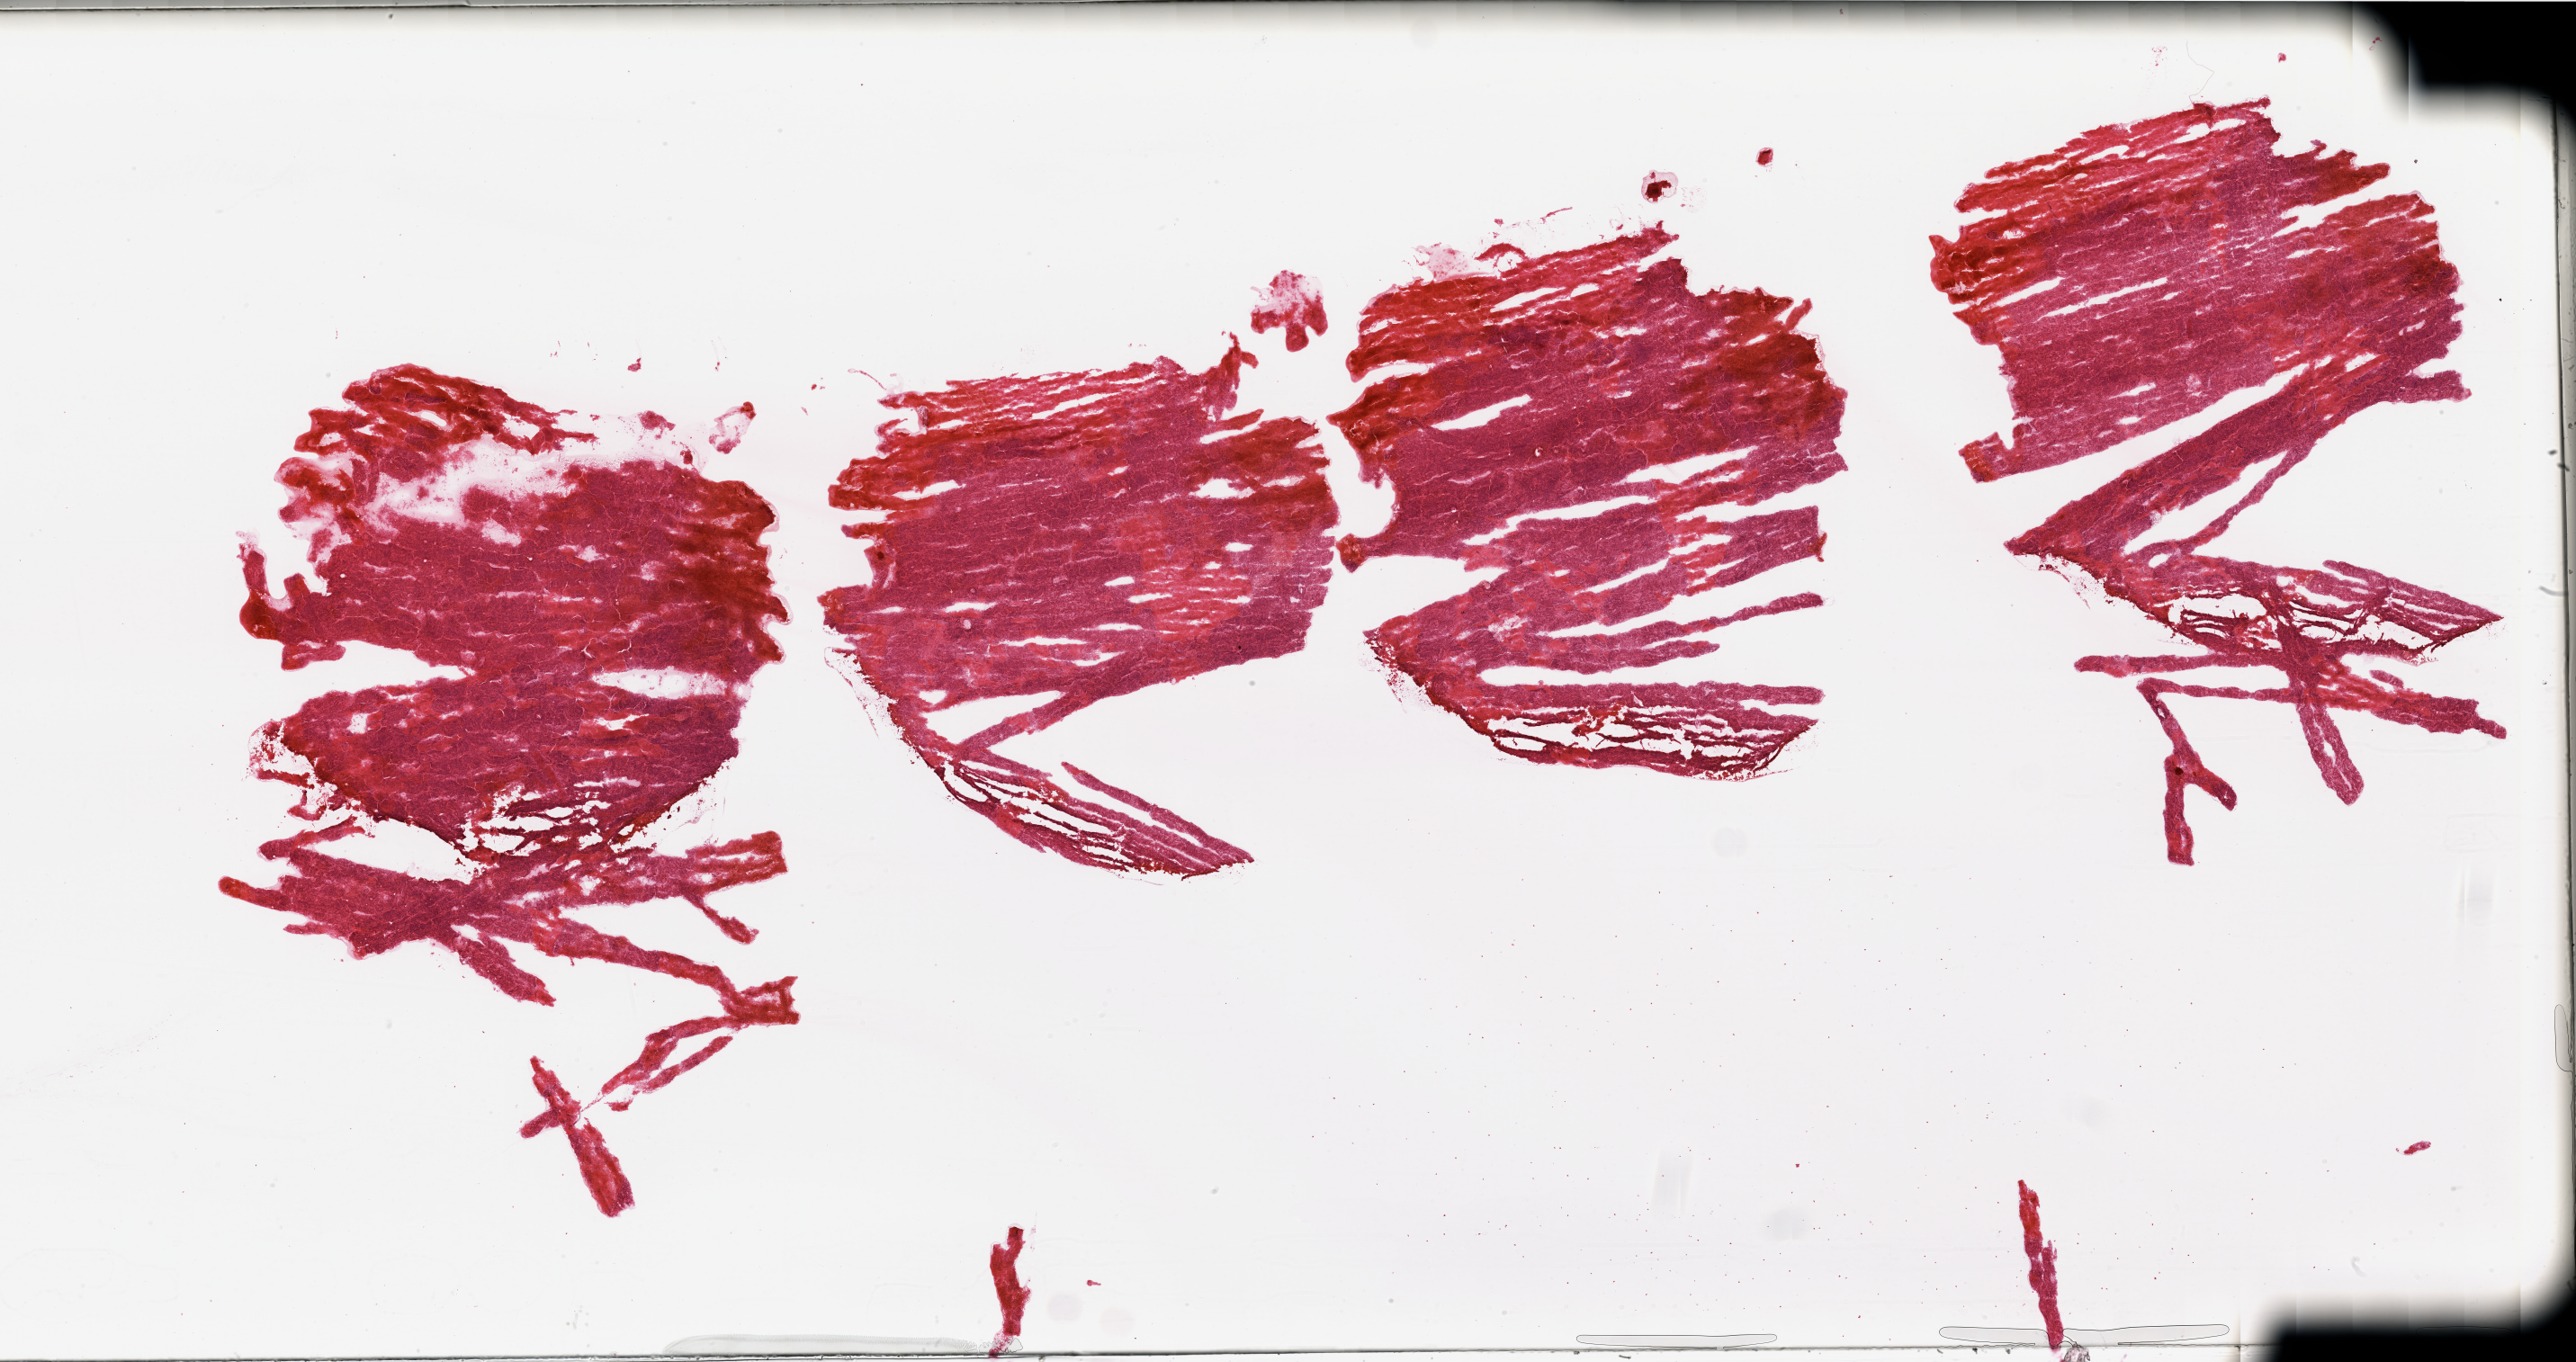
Hematoxylin and eosin (H&E) stained whole-slide image — low-resolution overview of the scanned area, about 45.3 x 23.9 mm (from a 20x scan); tumour tissue sample, kidney. Patient: female, age 49 years.
Histologic diagnosis: Renal cell carcinoma, NOS.